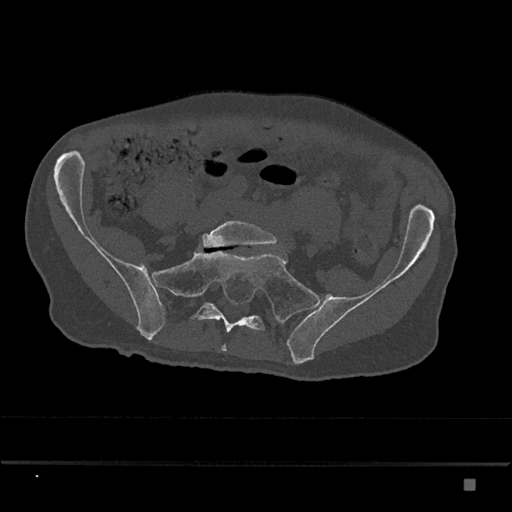
CT including the spine, one axial slice; position 224 of 797 along the scan axis; reconstruction kernel Br40s/3; bone window (W 1800 / L 400 HU); 0.5 mm slice thickness; 512 × 512 image matrix, field of view 390 × 390 mm. Male patient, age 72 years. Case-level facts recorded for this patient, not image findings: primary cancer: prostate.
Structures marked on this image (semi-automatic segmentation, software-assisted and operator-edited):
- L5 vertebra: box from (x=202, y=221) to (x=277, y=248) px